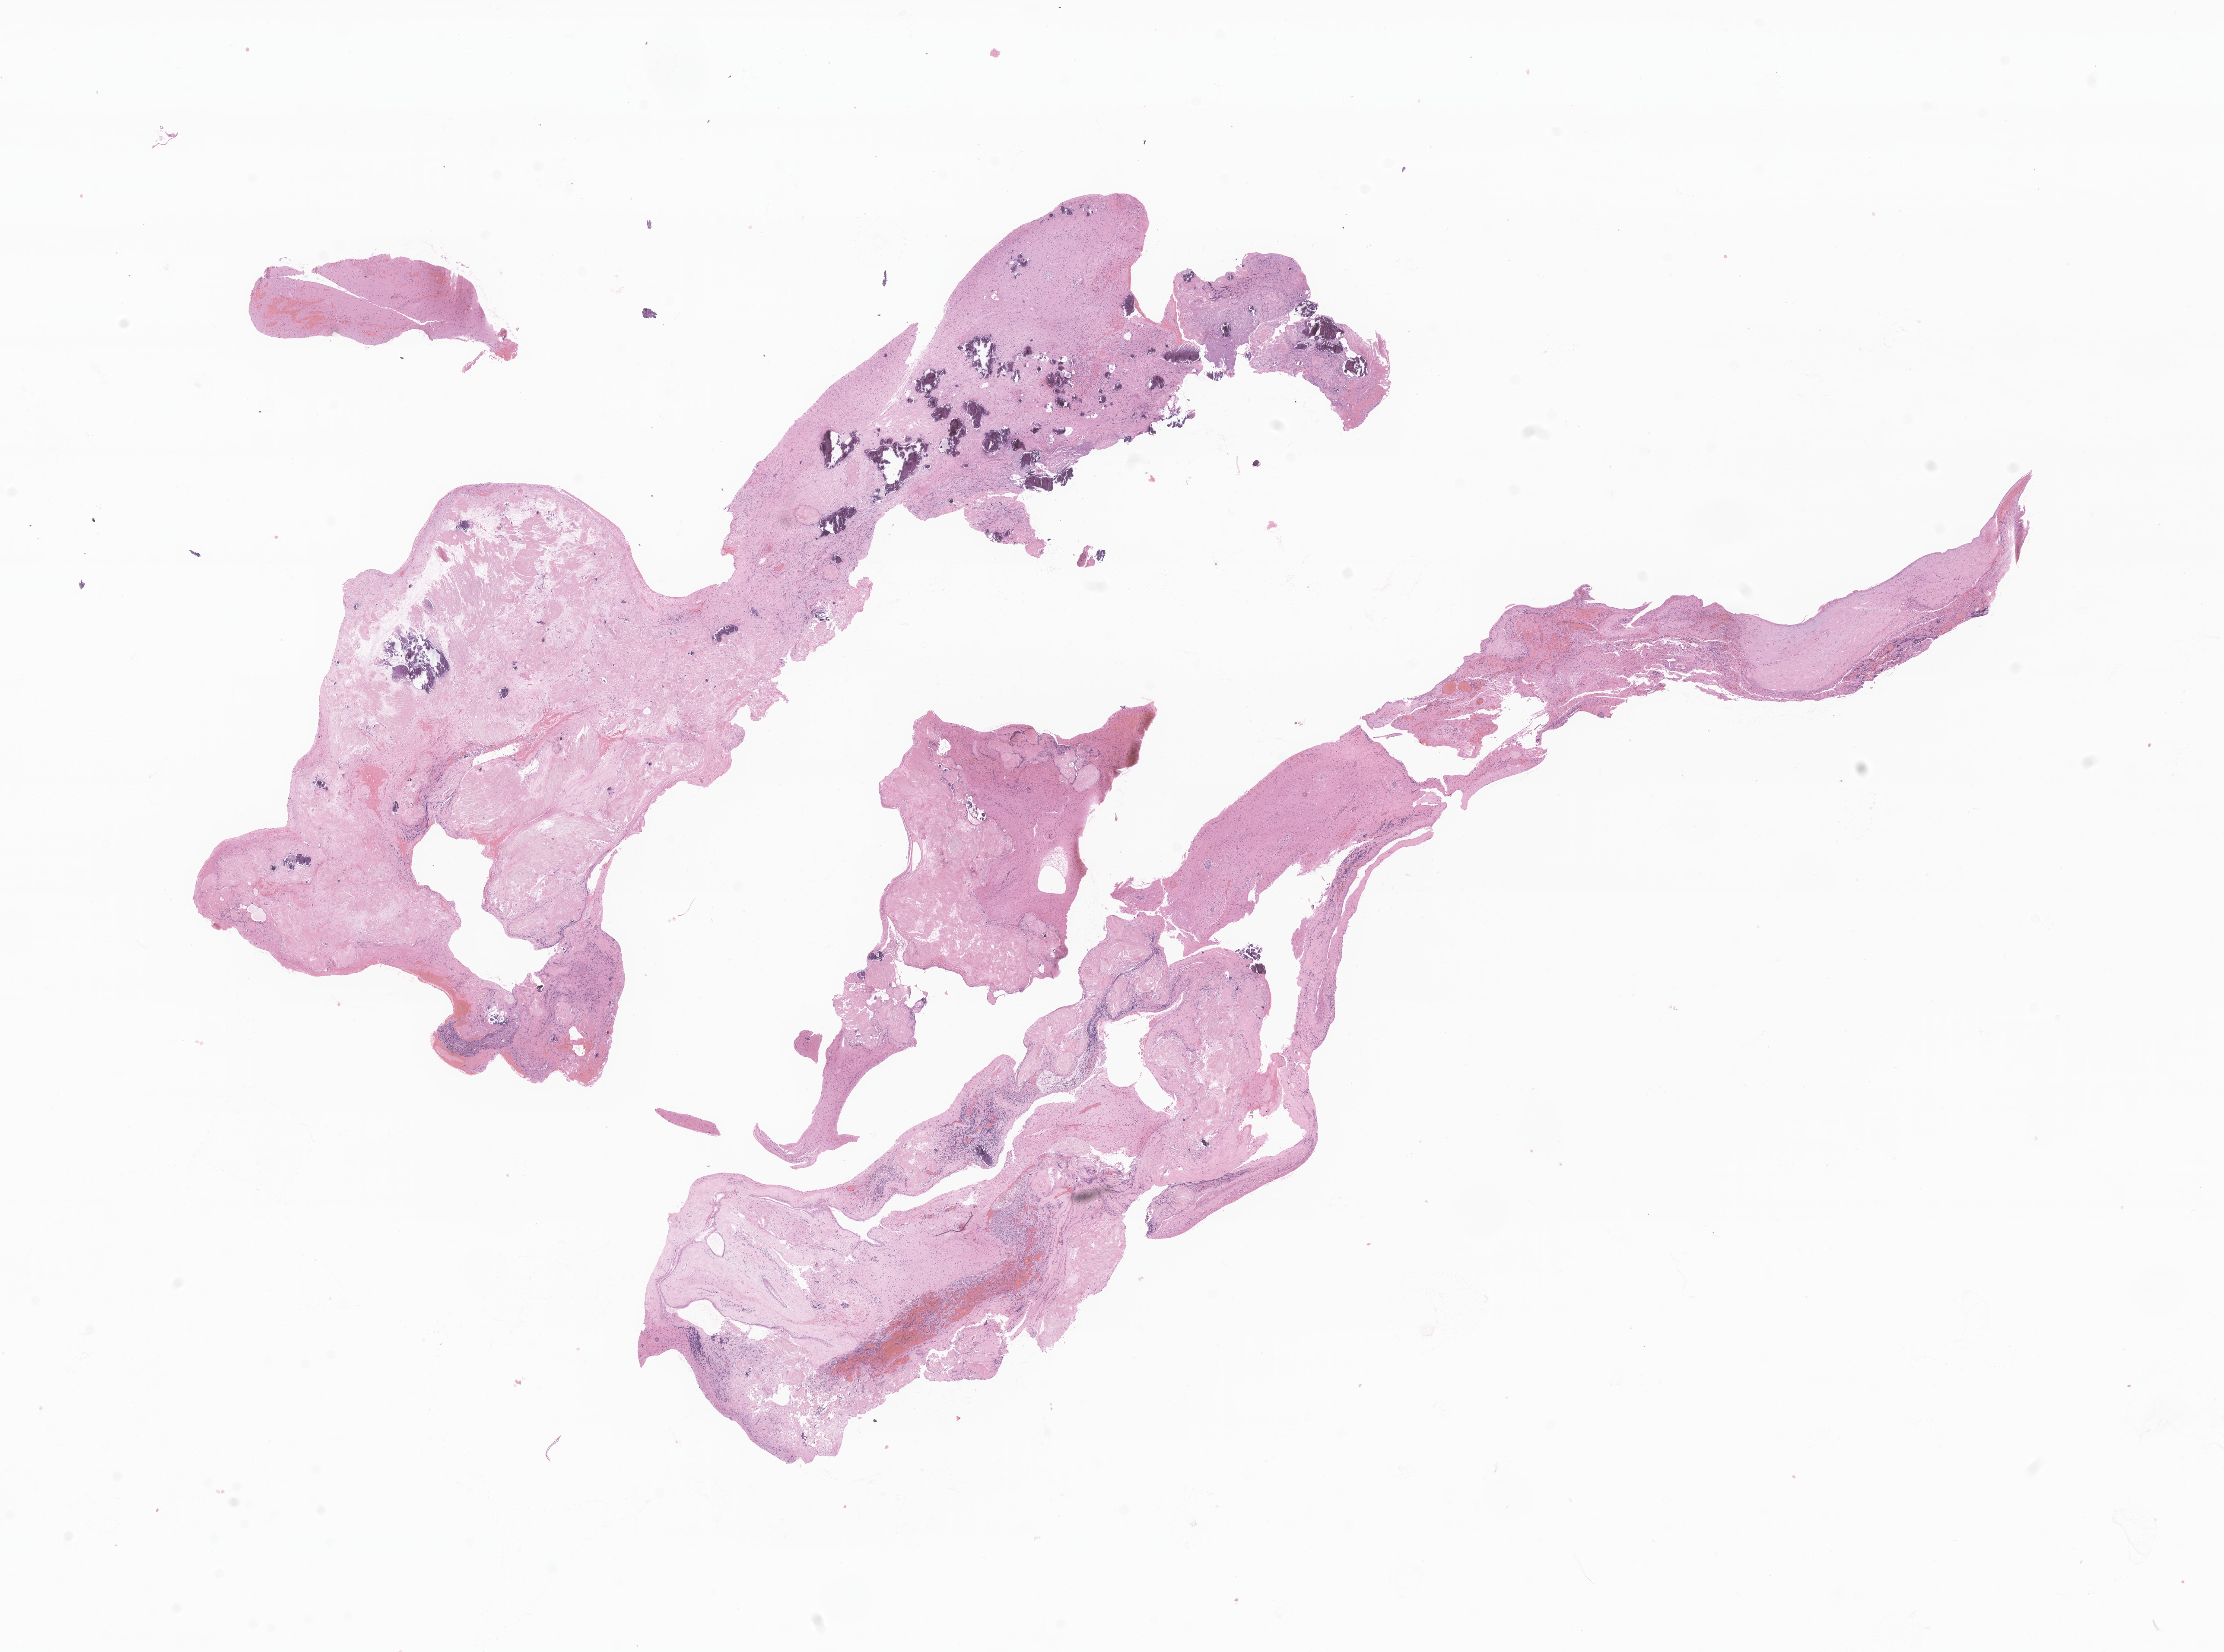
Digitized hematoxylin and eosin (H&E)-stained section of tumor tissue from the brain, shown as a low-resolution overview of the whole scanned area (about 21.7 x 16.1 mm), FFPE section. Patient: female, age 99 months (8 years 3 months).
Recorded diagnosis: Craniopharyngioma, adamantinomatous.